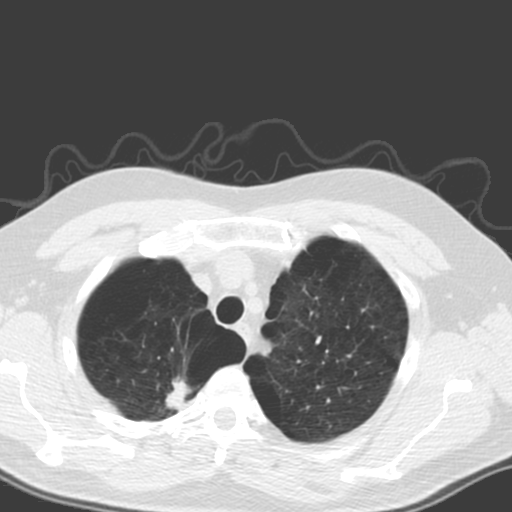
Chest CT (low-dose screening protocol), one axial image. Baseline screening round. Lung window (W 1500 / L -600 HU). 3.2 mm slice thickness. Standard (soft-tissue) reconstruction kernel (B). Slice 31 of 173 in the series. 512 × 512 image matrix. Male, age 56 years at enrolment. Former smoker at enrolment.
Expert reader's lesion annotation, bounding box [x1, y1, x2, y2] px = [139, 354, 209, 427]. Reader record for this screening exam (exam-level; its link to the box is not recorded): non-calcified nodule or mass ≥4 mm, right upper lobe, 20 × 12 mm, spiculated (stellate) margins, soft tissue attenuation. Later outcome: lung cancer diagnosed 205 days after this screen — large cell carcinoma, NOS, right upper lobe, poorly differentiated (G3), stage IA (AJCC 6th edition), 18 mm at pathology.